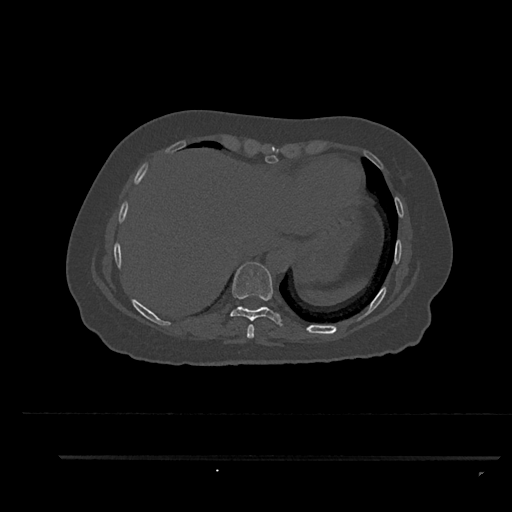
CT including the spine, one axial slice; slice 414 of 797 in the series (ordered by position); reconstruction kernel Br40s/3; 120 kVp; bone window (W 1800 / L 400 HU); 512 × 512 image matrix, field of view 408 × 408 mm. Female patient, age 44 years. From the clinical record (not read from this slice): primary cancer: renal; vertebrae with lytic lesions (as recorded): L1.
Structures marked on this image (semi-automatically segmented with operator editing):
- T8 vertebra: bounding box <247,324,255,339> (left, top, right, bottom; pixels)
- T9 vertebra: <230,262,283,327>